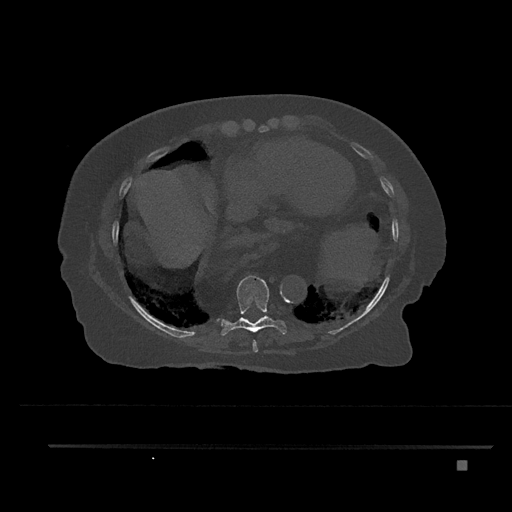
CT including the spine, one axial slice. Position 401 of 797 along the scan axis. Reconstruction kernel Br40s/3. 120 kVp. Bone window (W 1800 / L 400 HU). 0.5 mm slice thickness. 512 × 512 image matrix, field of view 437 × 437 mm. Patient: female, 76 years. Case-level facts recorded for this patient, not image findings: primary cancer: lung; vertebrae with lytic lesions (as recorded): T11, L3.
Outlined on this slice (semi-automatically segmented with operator editing):
- T8 vertebra: box from (x=252, y=340) to (x=258, y=352) px
- T9 vertebra: (x=220, y=276)–(x=287, y=336)